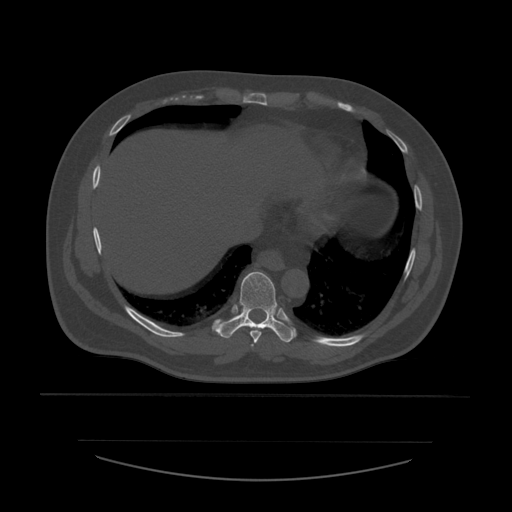
CT including the spine, one axial slice; position 322 of 532 along the scan axis; 120 kVp; bone window (W 1800 / L 400 HU); 1.25 mm slice thickness; 512 × 512 image matrix. Patient age 44 years. Case-level facts recorded for this patient, not image findings: primary cancer: soft tissue sarcoma.
Structures marked on this image (semi-automatically segmented with operator editing):
- T7 vertebra: bounding box <251,344,254,347> (left, top, right, bottom; pixels)
- T8 vertebra: <250,331,262,344>
- T9 vertebra: <216,272,296,343>